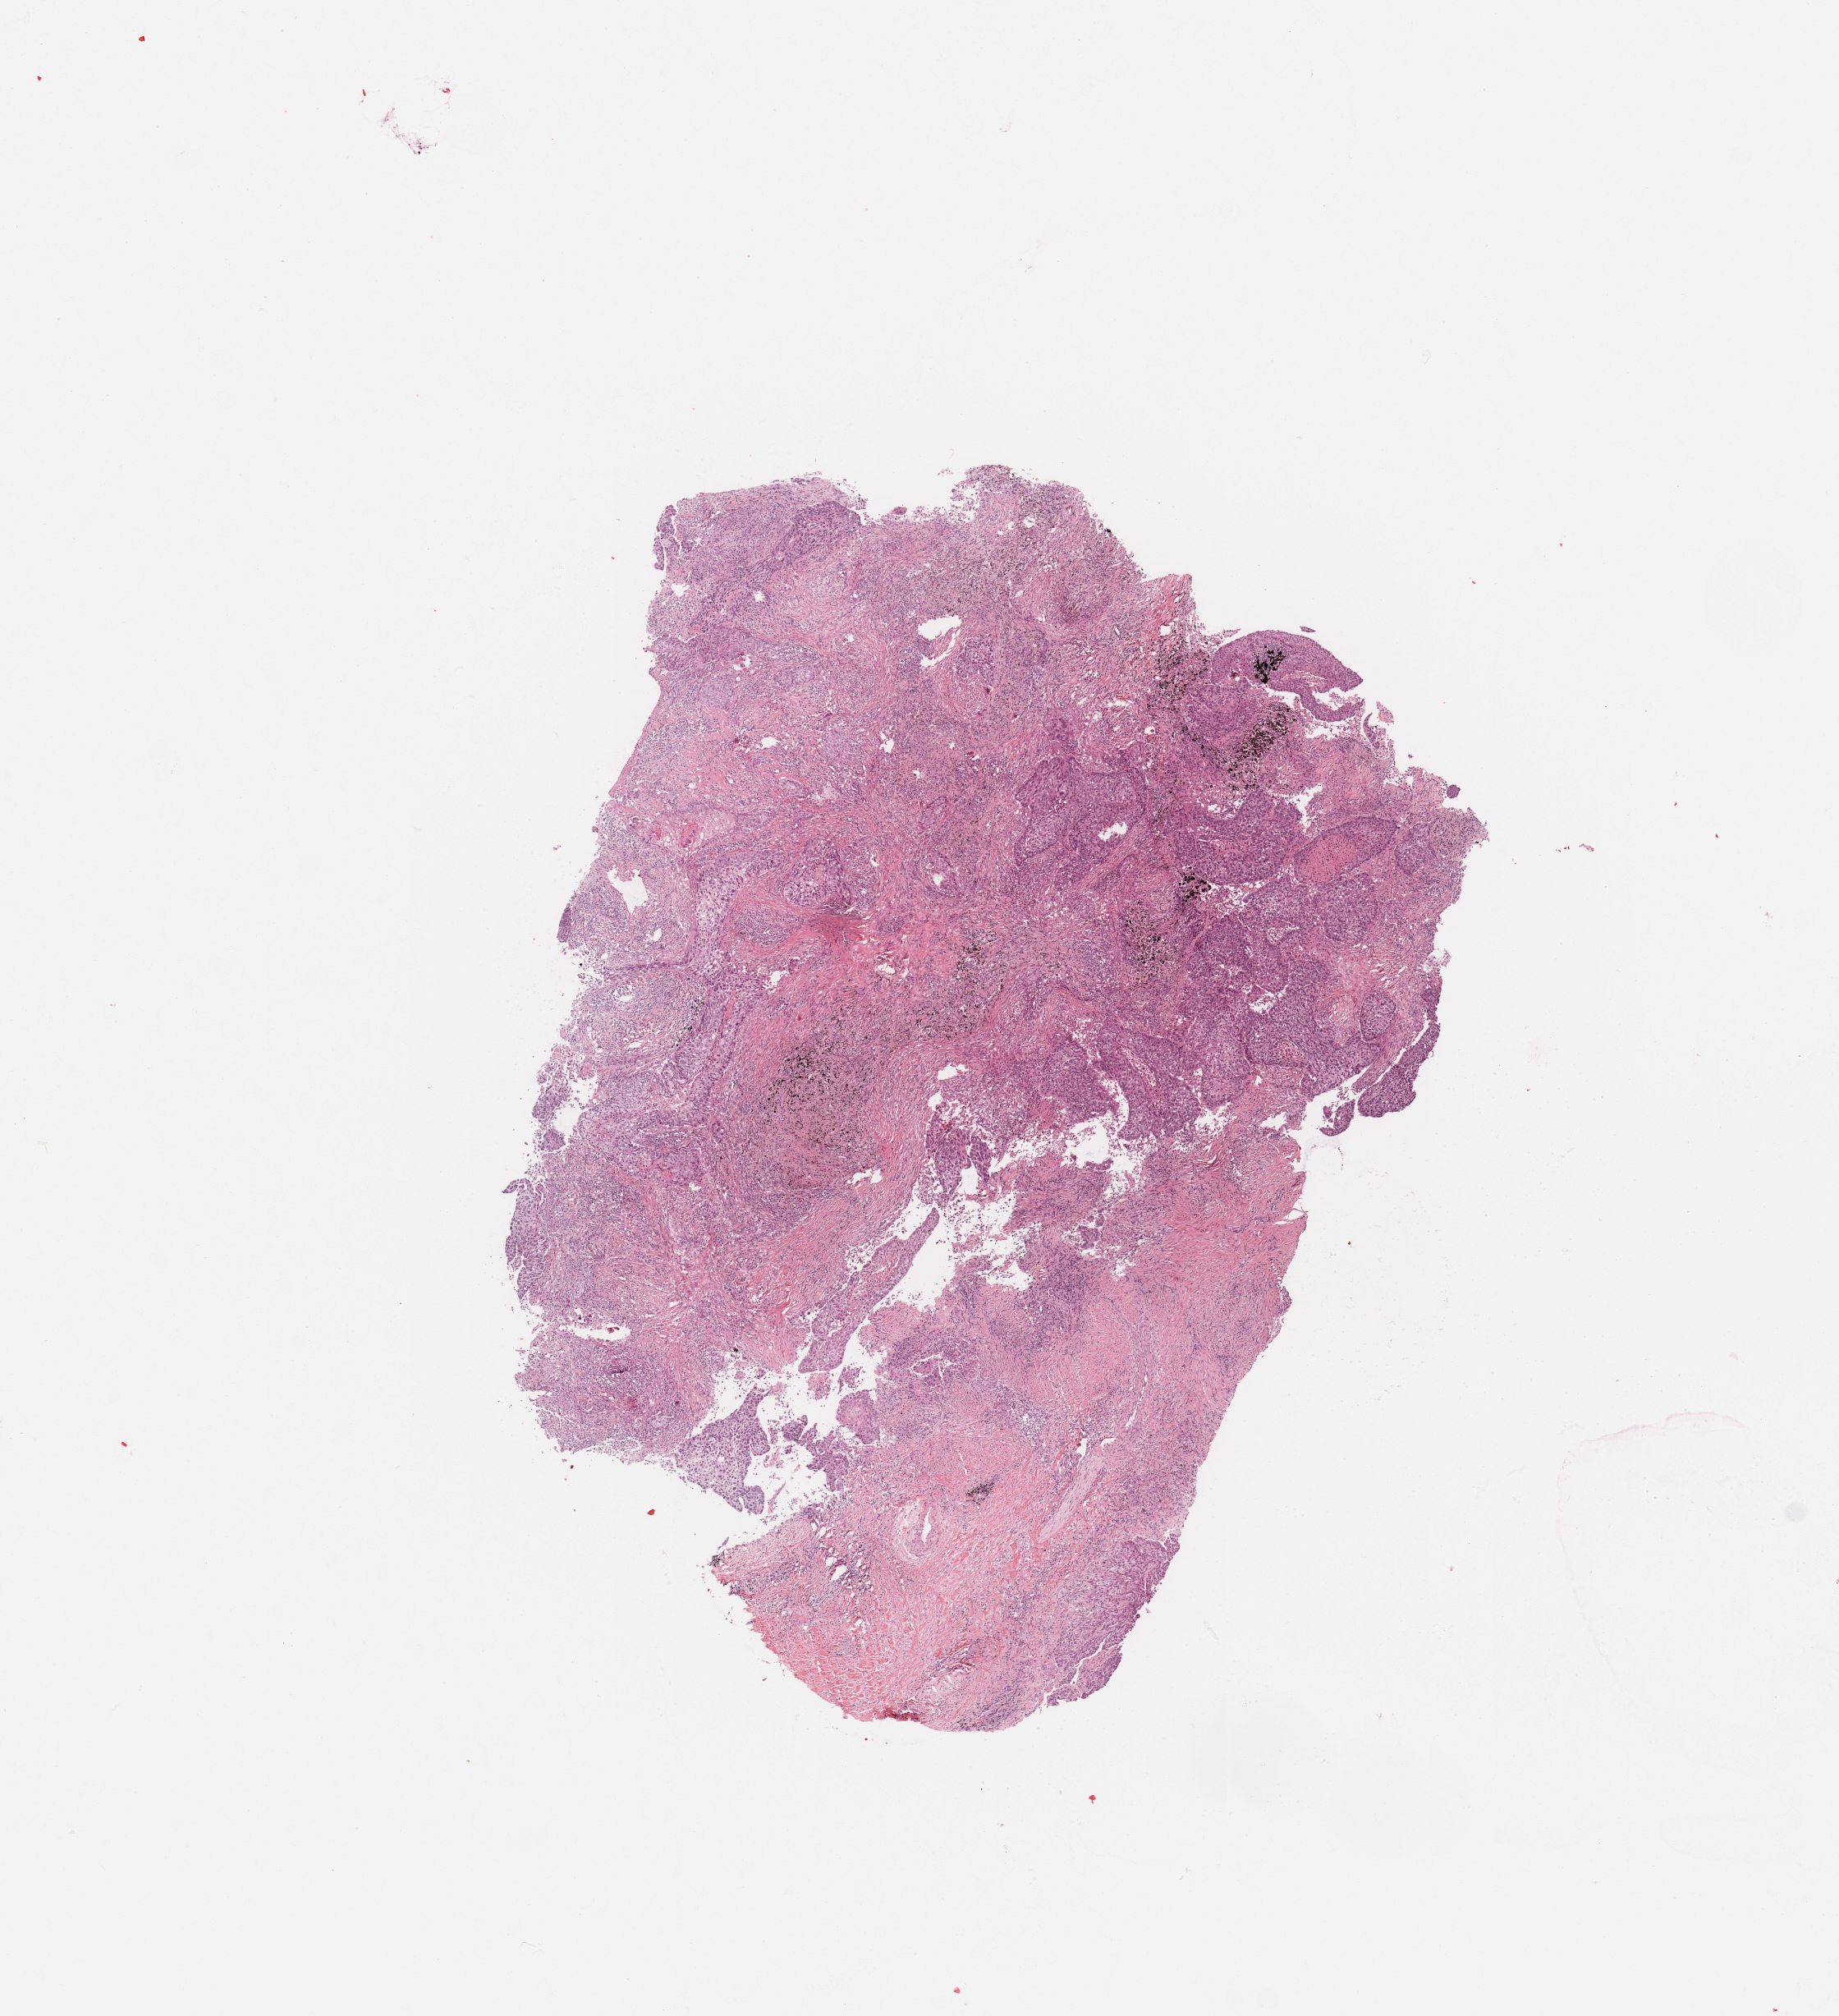
Whole-slide histology image, H&E, a low-resolution overview of the entire scanned area, about 8.9 x 9.7 mm (from a 20x scan). Tumour tissue sample, sampled site: lung. Patient: male, age 62 years. Histologic grade: G3 (poorly differentiated). Slide review estimates, as recorded: tumour nuclei 65%, necrosis 5%.
- AJCC pathologic stage: IB
- primary tumour site (as recorded): left upper lobe
- histologic diagnosis: Squamous cell carcinoma, NOS